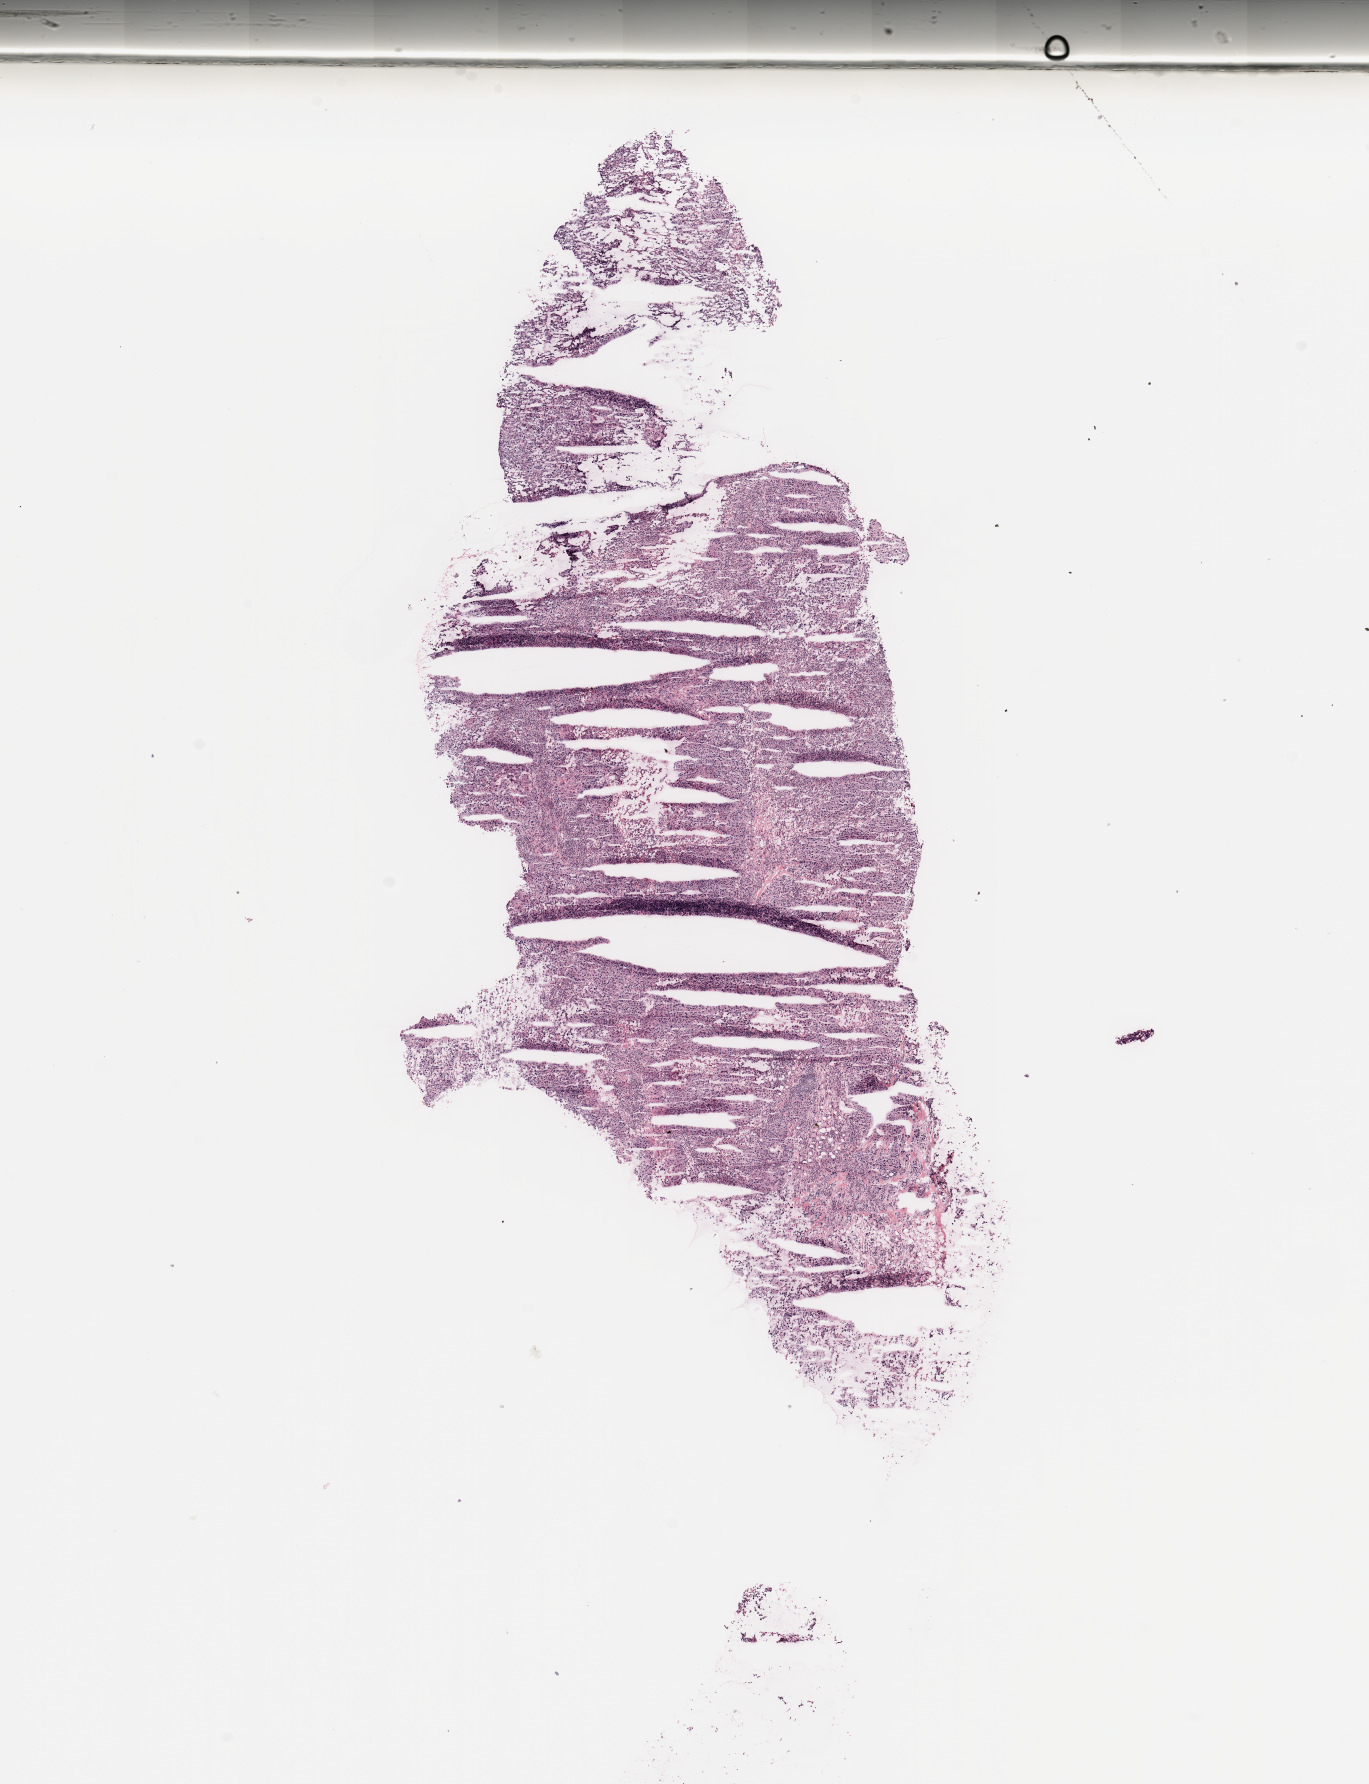
Digitized H&E-stained tissue section (whole slide) — low-resolution overview of the scanned area, about 10.8 x 14.1 mm (slide scanned at 20x). Tumour tissue sample, breast. Patient: female, age 40 years.
AJCC pathologic stage: IIB. Histologic diagnosis: Infiltrating duct carcinoma, NOS.